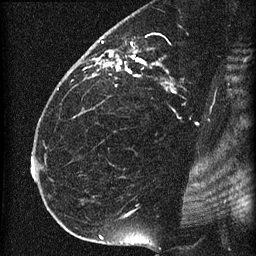
Breast MRI (dynamic contrast-enhanced), one sagittal slice; dynamic contrast-enhanced series, image 2 of 4 at this slice position (ordered by acquisition); 1.5 T; TE 4.2 ms, TR 22.7 ms; 256 × 256 image matrix, field of view 180 × 180 mm. Female patient, age 35 years. From the clinical record (not read from this slice): setting: breast cancer imaged before/during neoadjuvant chemotherapy; receptor status: HR-positive, HER2-negative.
Structures marked on this image (semi-automatic segmentation, software-assisted and operator-edited):
- analysis volume of interest (the breast-tissue region the enhancement analysis was run in; not a lesion): bounding box [x1, y1, x2, y2] px = [69, 27, 196, 112]
- tumour enhancement mask (voxels above the 90 % enhancement threshold inside the analysis volume of interest): [93, 41, 173, 85]